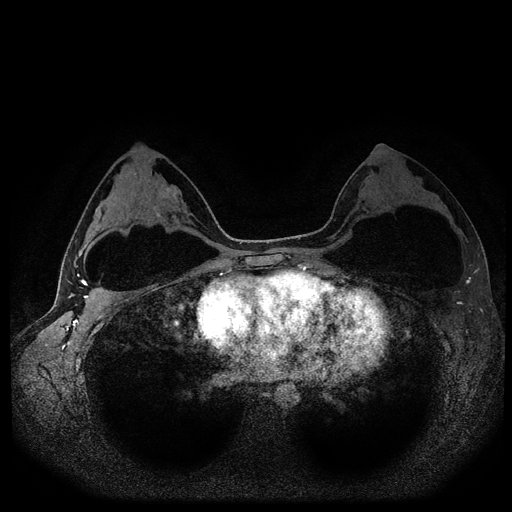
Breast MRI (dynamic contrast-enhanced, multi-phase), one axial slice. Slice 61 of 116 in the series (ordered by position). Dynamic contrast-enhanced series, time point 2 of 5 at this slice position (early post-contrast). 1.5 T. TE 2.6 ms, TR 5.4 ms. 512 × 512 image matrix, field of view 340 × 340 mm. Female patient, age 33 years.
Annotated regions visible in this slice (semi-automatically segmented with operator editing):
- breast lesion (labelled benign in the annotation): bounding box <159,185,182,204> (left, top, right, bottom; pixels)